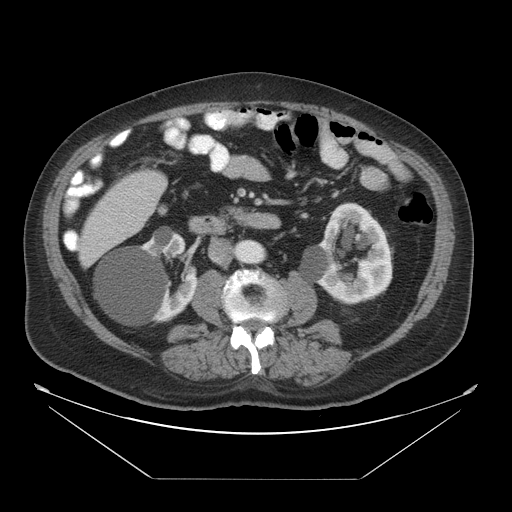
Contrast-enhanced abdominal CT, one axial slice; position 13 of 45 along the scan axis; intravenous contrast given; soft-tissue window (W 400 / L 40 HU); 5 mm slice thickness; 512 × 512 image matrix, field of view 463 × 463 mm. Male patient, age 87 years. Case-level facts recorded for this patient, not image findings: diagnosis: colorectal cancer liver metastases, imaged before liver resection; multiple liver metastases: no; largest metastasis: 4.5 cm; chemotherapy before resection: no.
Outlined on this slice (expert manual segmentation):
- liver: bounding box <79,169,168,268> (left, top, right, bottom; pixels)